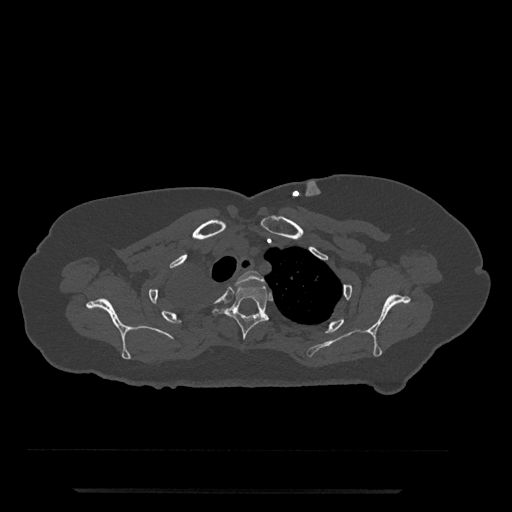
CT including the spine, one axial slice; position 635 of 797 along the scan axis; reconstruction kernel Br40s/3; bone window (W 1800 / L 400 HU); 0.5 mm slice thickness; 512 × 512 image matrix. Female patient, age 51 years. Case-level facts recorded for this patient, not image findings: primary cancer: neuro.
Outlined on this slice (semi-automatic segmentation, software-assisted and operator-edited):
- T2 vertebra: bounding box <227,271,265,302> (left, top, right, bottom; pixels)
- T3 vertebra: <213,284,269,340>